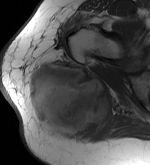
MRI of an extremity soft-tissue mass, one axial slice. Slice 33 of 56 in the series (ordered by position). MR volume resampled by the dataset authors to the PET/CT grid (not the native acquisition matrix). 150 × 165 image matrix, field of view 146 × 161 mm. Female patient. From the clinical record (not read from this slice): histological type: epithelioid sarcoma with vascular differentiation; site of the primary tumour: right buttock.
Outlined on this slice (expert contour drawn on MRI and transferred to this co-registered scan by the dataset authors):
- gross tumour volume (mass): bounding box <25,60,111,139> (left, top, right, bottom; pixels)